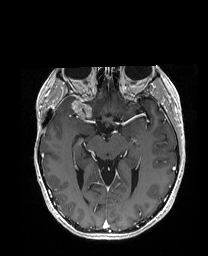
Brain MRI from a brain-tumour surgery series, one axial slice; slice 105 of 192 in the series (ordered by position); T1-weighted post-contrast; 208 × 256 image matrix, field of view 203 × 250 mm. From the clinical record (not read from this slice): histopathology: Metastatic Carcinoma from Breast primary; tumour location: Right Frontal.
Annotated regions visible in this slice (expert manual segmentation):
- tumour: bounding box <61,98,81,117> (left, top, right, bottom; pixels)